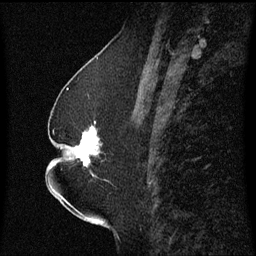
Breast MRI (dynamic contrast-enhanced), one sagittal slice. Position 27 of 60 along the scan axis. Dynamic contrast-enhanced series, image 2 of 3 at this slice position (ordered by acquisition). 1.5 T. TE 4.2 ms, TR 8.4 ms. 256 × 256 image matrix, field of view 200 × 200 mm. Female patient, age 52 years. From the clinical record (not read from this slice): setting: breast cancer imaged before/during neoadjuvant chemotherapy; receptor status: HR-positive, HER2-negative.
Annotated regions visible in this slice (semi-automatic segmentation, software-assisted and operator-edited):
- analysis volume of interest (the breast-tissue region the enhancement analysis was run in; not a lesion): bounding box [x1, y1, x2, y2] px = [65, 122, 110, 183]
- tumour enhancement mask (voxels above the 70 % enhancement threshold inside the analysis volume of interest): [75, 126, 100, 165]